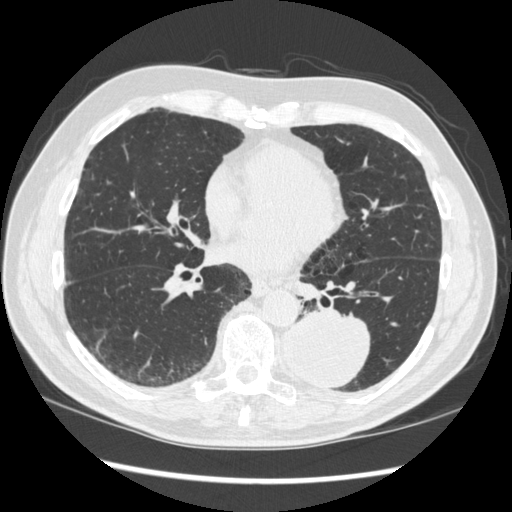
Low-dose screening chest CT, one axial slice. Slice 143 of 348 in the series (ordered by position). 120 kVp. Lung window (W 1500 / L -600 HU). 1.25 mm slice thickness. 512 × 512 image matrix, field of view 360 × 360 mm.
Outlined on this slice (expert manual segmentation):
- lesion 1 (tumor, lower lobe of left lung): bounding box [x1, y1, x2, y2] px = [283, 311, 370, 390]